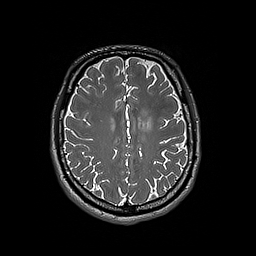
Brain MRI from a brain-tumour surgery series, one axial slice; slice 66 of 192 in the series (ordered by position); 1 mm slice thickness; 256 × 256 image matrix, field of view 250 × 250 mm. From the clinical record (not read from this slice): histopathology: Oligodendroglioma; WHO grade: 3; IDH mutation: yes; tumour location: Left Frontal.
Structures marked on this image (outlined manually by an expert reader):
- tumour: box from (x=138, y=118) to (x=153, y=130) px